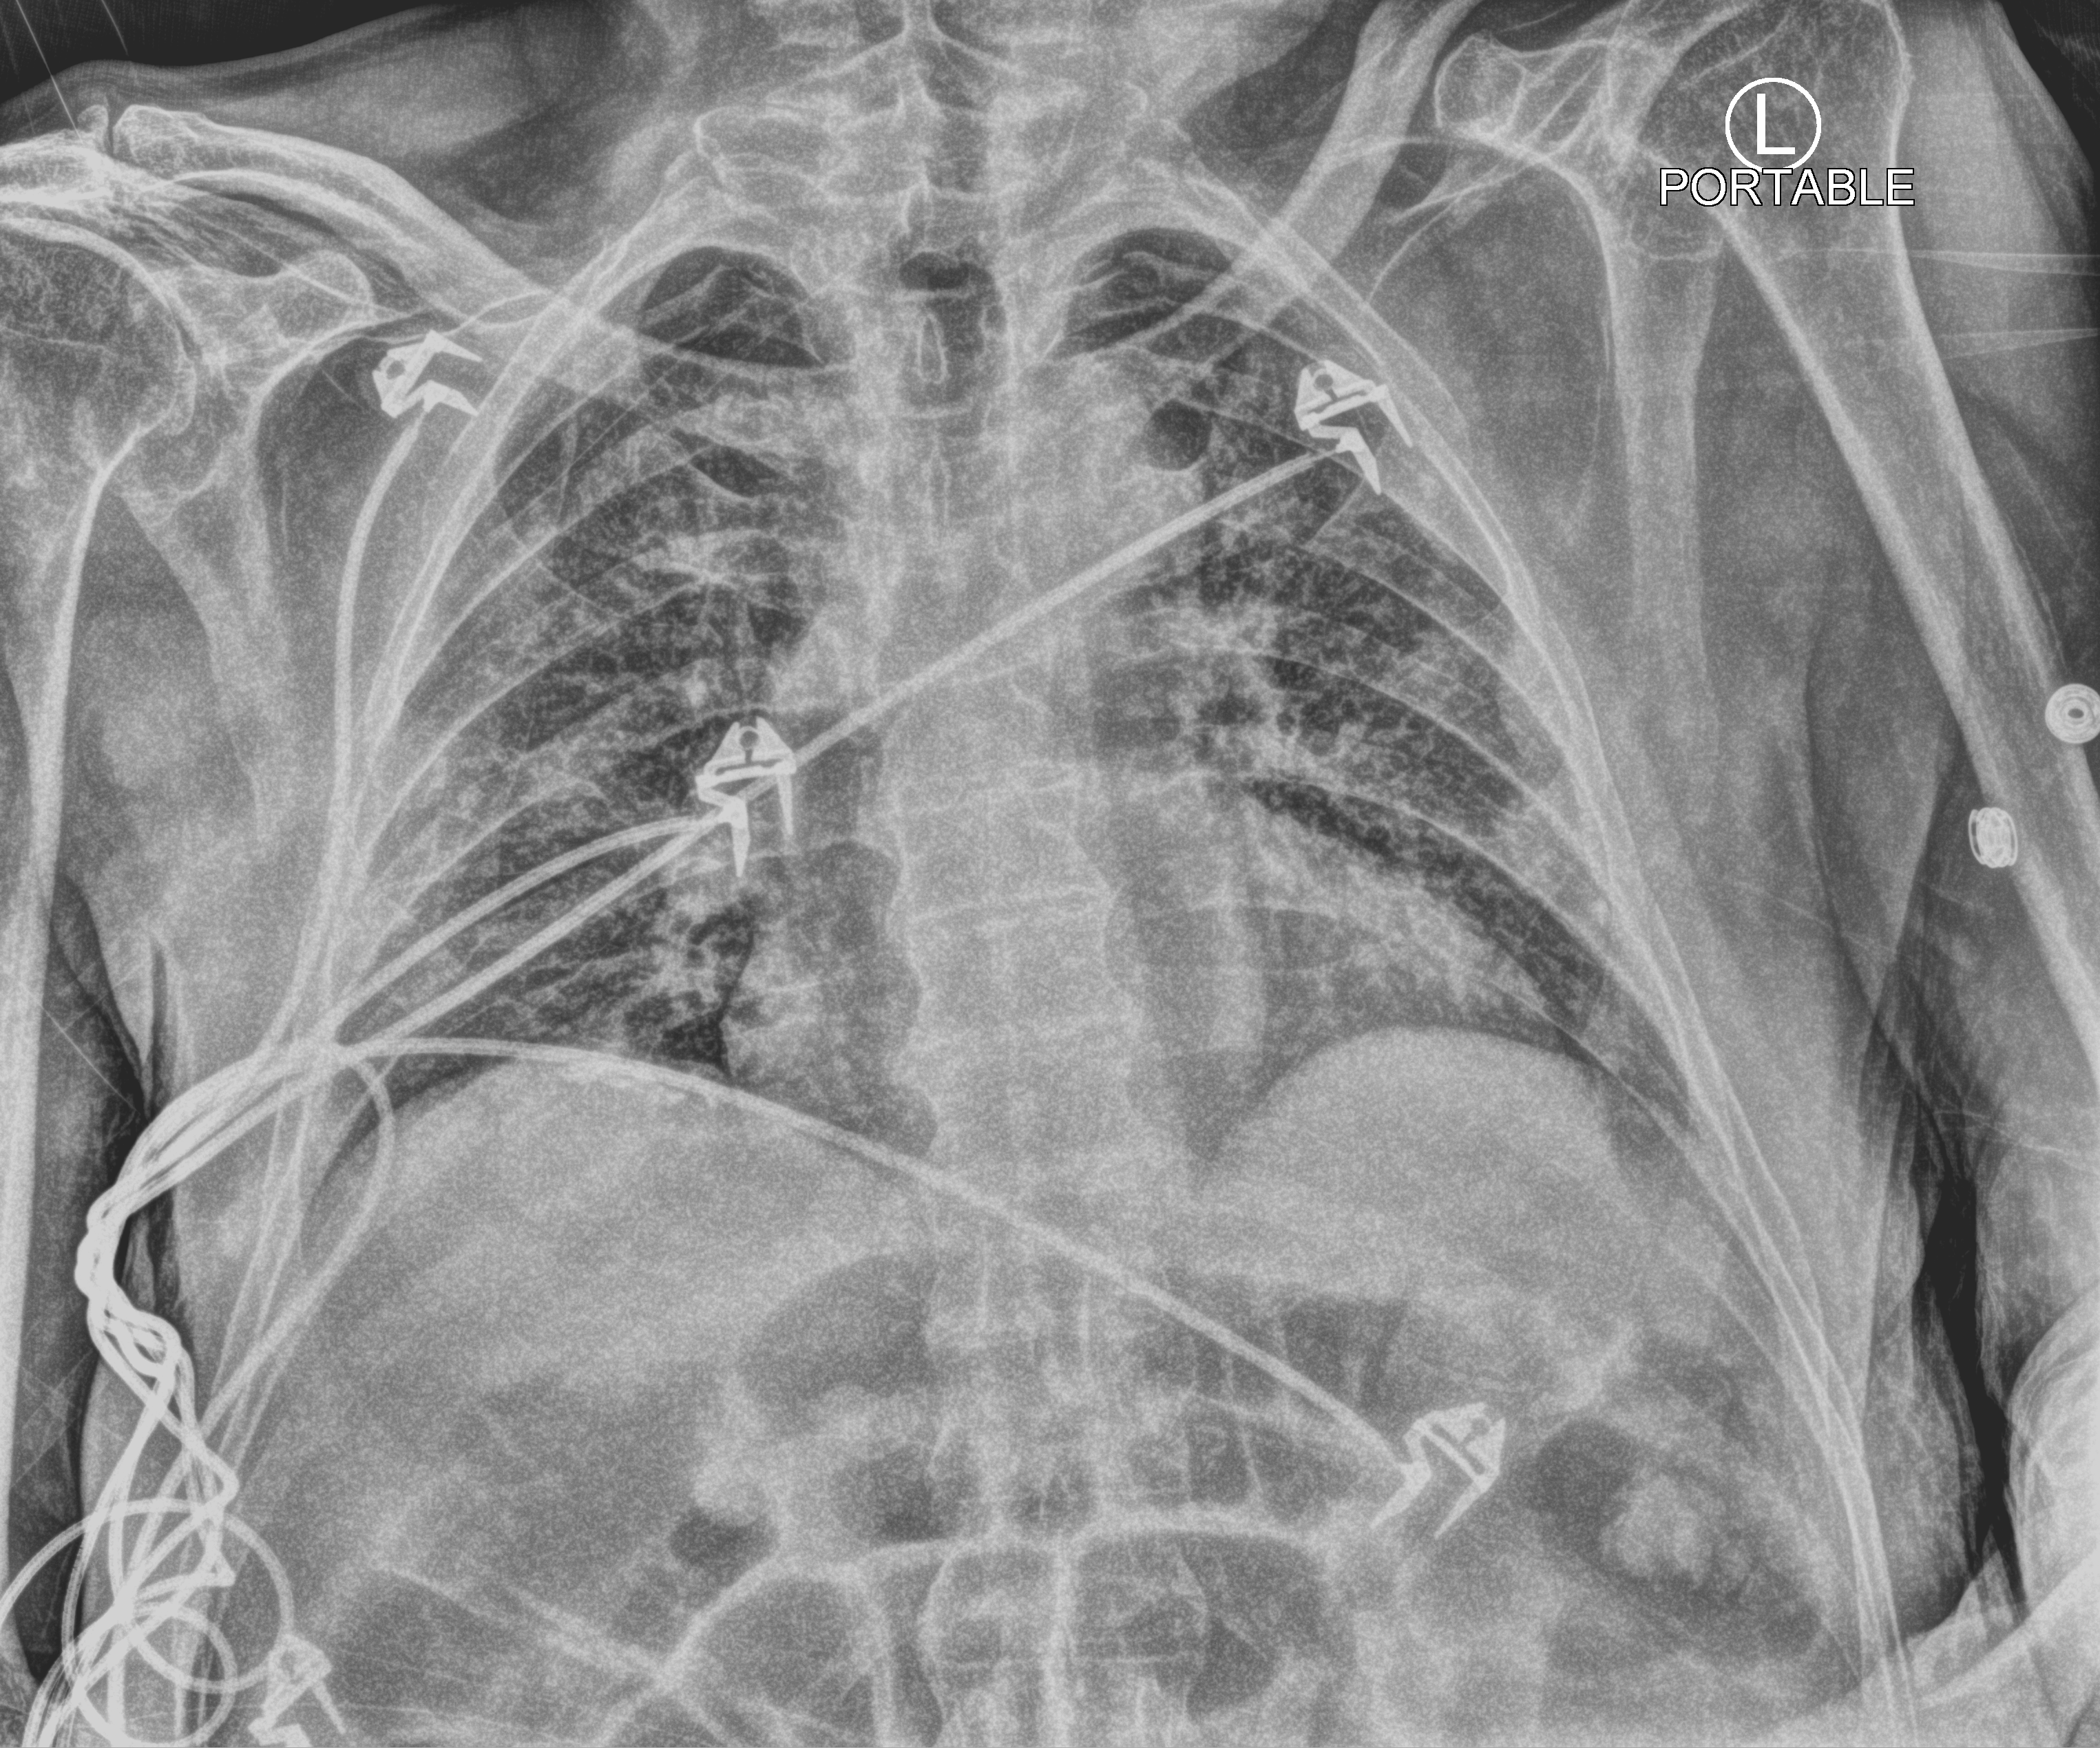
Chest X-ray (portable); anteroposterior (AP) projection. Male patient hospitalised with COVID-19, age 75–90 years.
Admission-level facts for this patient (not findings on this image; timing relative to this image not recorded): length of hospital stay: 1 day; mechanically ventilated during this hospital stay: no.